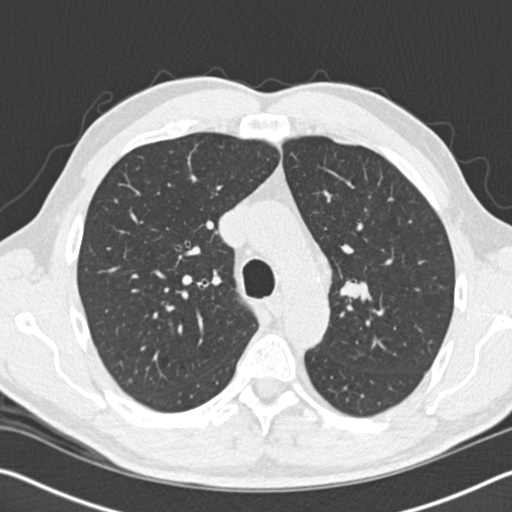
Low-dose screening chest CT, axial slice. First (baseline) screen. Lung window (W 1500 / L -600 HU). 2 mm slice thickness. Slice 55 of 162 in the series. 512 × 512 image matrix, field of view 340 × 340 mm. Male, age 61 years at enrolment.
• Expert reader's lesion annotation, bounding box [x1, y1, x2, y2] px = [342, 273, 373, 315].
• The screening reader recorded 2 non-calcified nodules or masses ≥4 mm on this exam (right middle lobe, left upper lobe); which of them this box marks is not recorded.